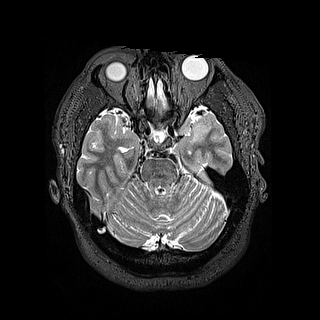
Brain MRI from a brain-tumour surgery series, one axial slice; position 105 of 144 along the scan axis; 320 × 320 image matrix. From the clinical record (not read from this slice): histopathology: Astrocytoma; WHO grade: 2; IDH mutation: yes; tumour location: Left Insular.
Outlined on this slice (manually delineated by an expert):
- tumour: bounding box (x1, y1, x2, y2) in pixels: (188, 125, 202, 144)